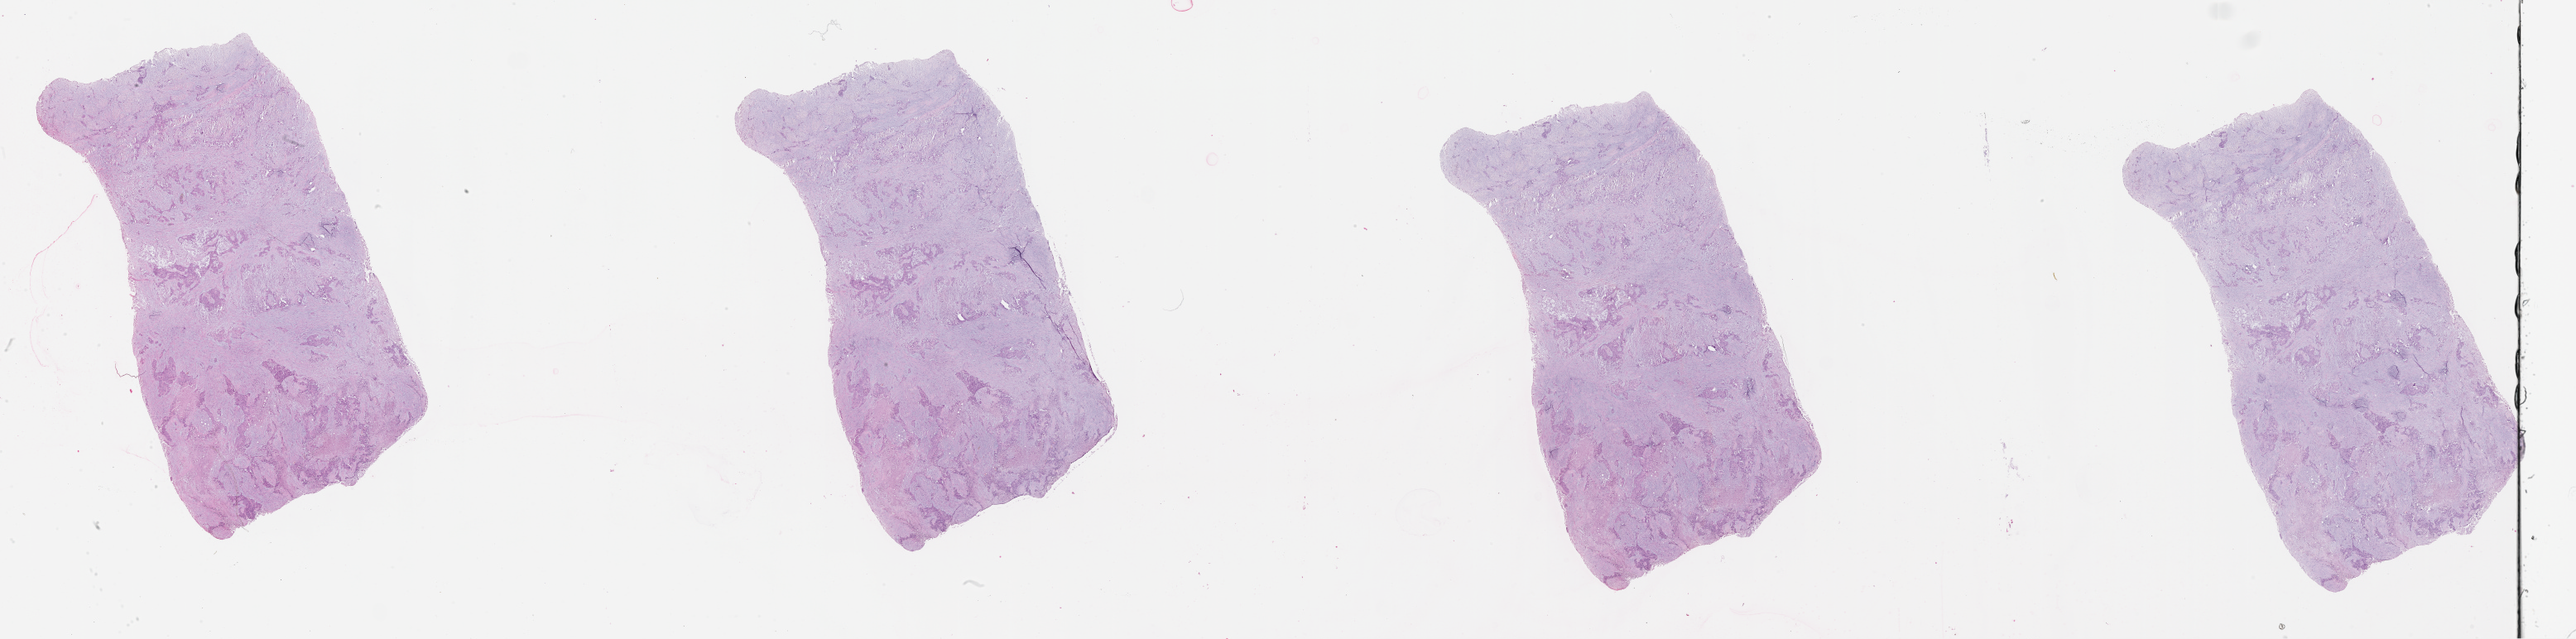
Whole-slide histology image, H&E-stained — shown as a low-resolution overview of the whole scanned area (about 50.1 x 12.4 mm, acquisition: 20x scan); lung, tumour tissue. 74-year-old male patient.
Patient diagnosis (cohort enrolment): squamous cell carcinoma (lung).